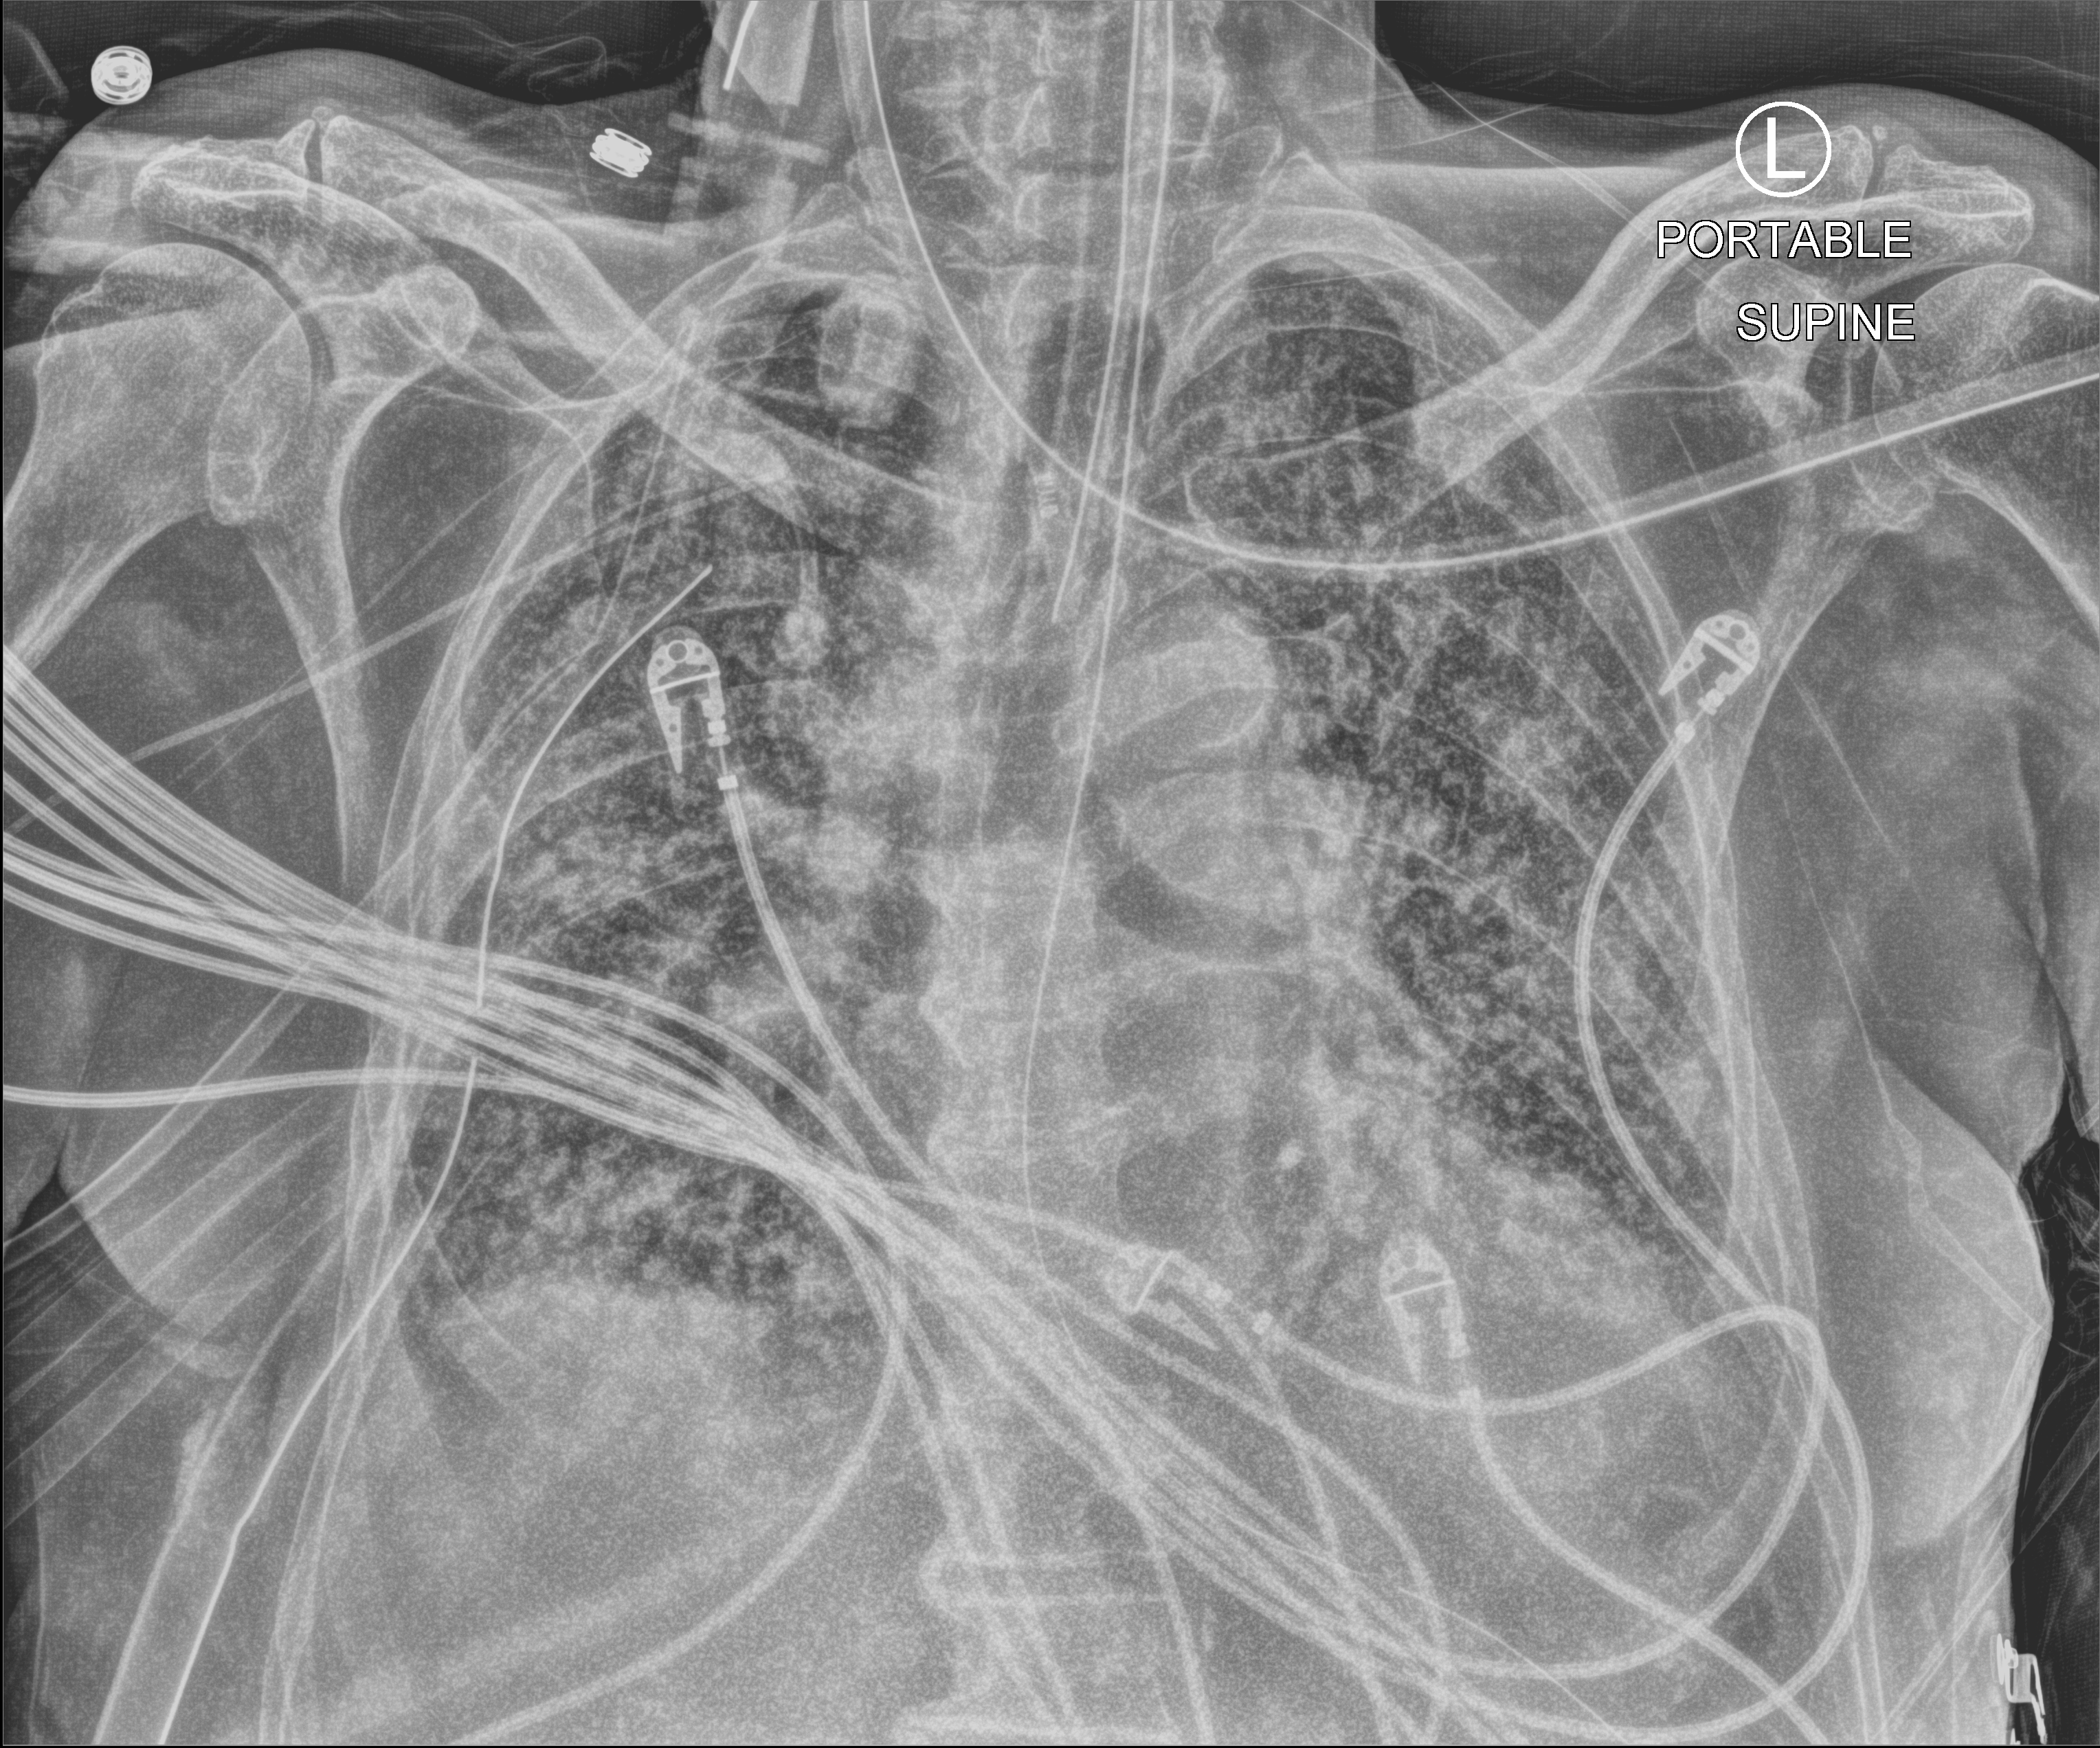
Portable chest radiograph; anteroposterior (AP) projection. Patient hospitalised with COVID-19; male, aged 75–90 years.
From the hospital-stay record, not from the radiograph (when in the stay this image was taken is not recorded):
- length of hospital stay: 47 days